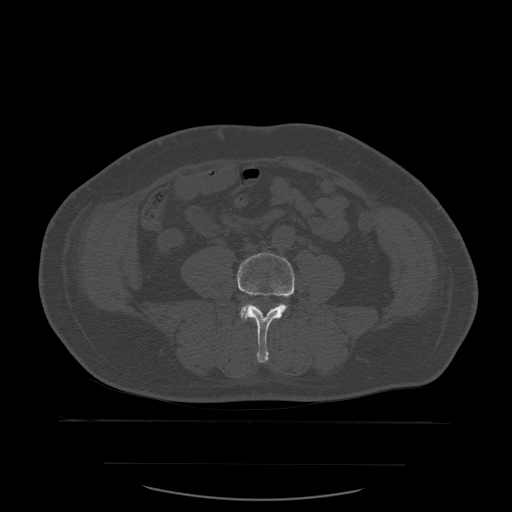
CT including the spine, one axial slice. Position 161 of 590 along the scan axis. Bone window (W 1800 / L 400 HU). 1.25 mm slice thickness. 512 × 512 image matrix, field of view 479 × 479 mm. Patient age 71 years. Case-level facts recorded for this patient, not image findings: primary cancer: lung; vertebrae with lytic lesions (as recorded): T1, T2, L5, S1.
Outlined on this slice (semi-automatically segmented with operator editing):
- L4 vertebra: bounding box <237,253,295,363> (left, top, right, bottom; pixels)
- L5 vertebra: <241,302,279,315>